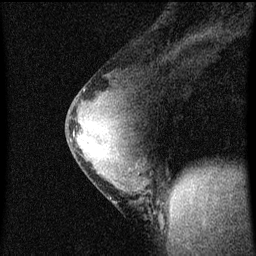
Breast MRI (dynamic contrast-enhanced), one sagittal slice. Slice 34 of 60 in the series (ordered by position). Dynamic contrast-enhanced series, image 2 of 4 at this slice position (ordered by acquisition). 1.5 T. TE 4.2 ms, TR 8 ms. 256 × 256 image matrix. Patient: female, 33 years.
Structures marked on this image (semi-automatic segmentation, software-assisted and operator-edited):
- analysis volume of interest (the breast-tissue region the enhancement analysis was run in; not a lesion): box from (x=67, y=76) to (x=161, y=219) px
- tumour enhancement mask (voxels above the 70 % enhancement threshold inside the analysis volume of interest): (x=76, y=116)–(x=84, y=149)